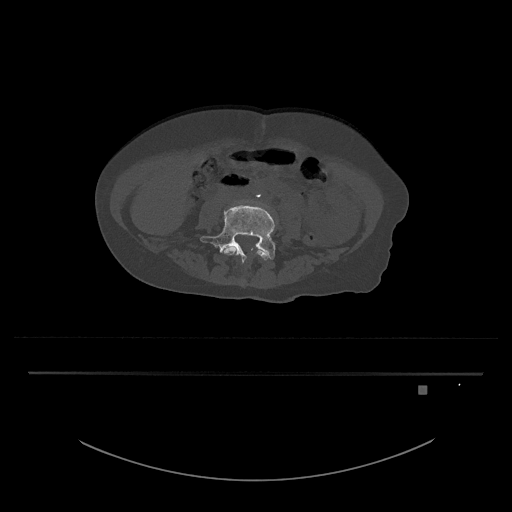
CT including the spine, one axial slice; slice 322 of 797 in the series (ordered by position); reconstruction kernel Br40s/3; bone window (W 1800 / L 400 HU); 0.5 mm slice thickness; 512 × 512 image matrix, field of view 500 × 500 mm. Female patient, age 57 years. From the clinical record (not read from this slice): primary cancer: cervical.
Annotated regions visible in this slice (semi-automatic segmentation, software-assisted and operator-edited):
- L4 vertebra: bounding box [x1, y1, x2, y2] px = [224, 246, 271, 260]